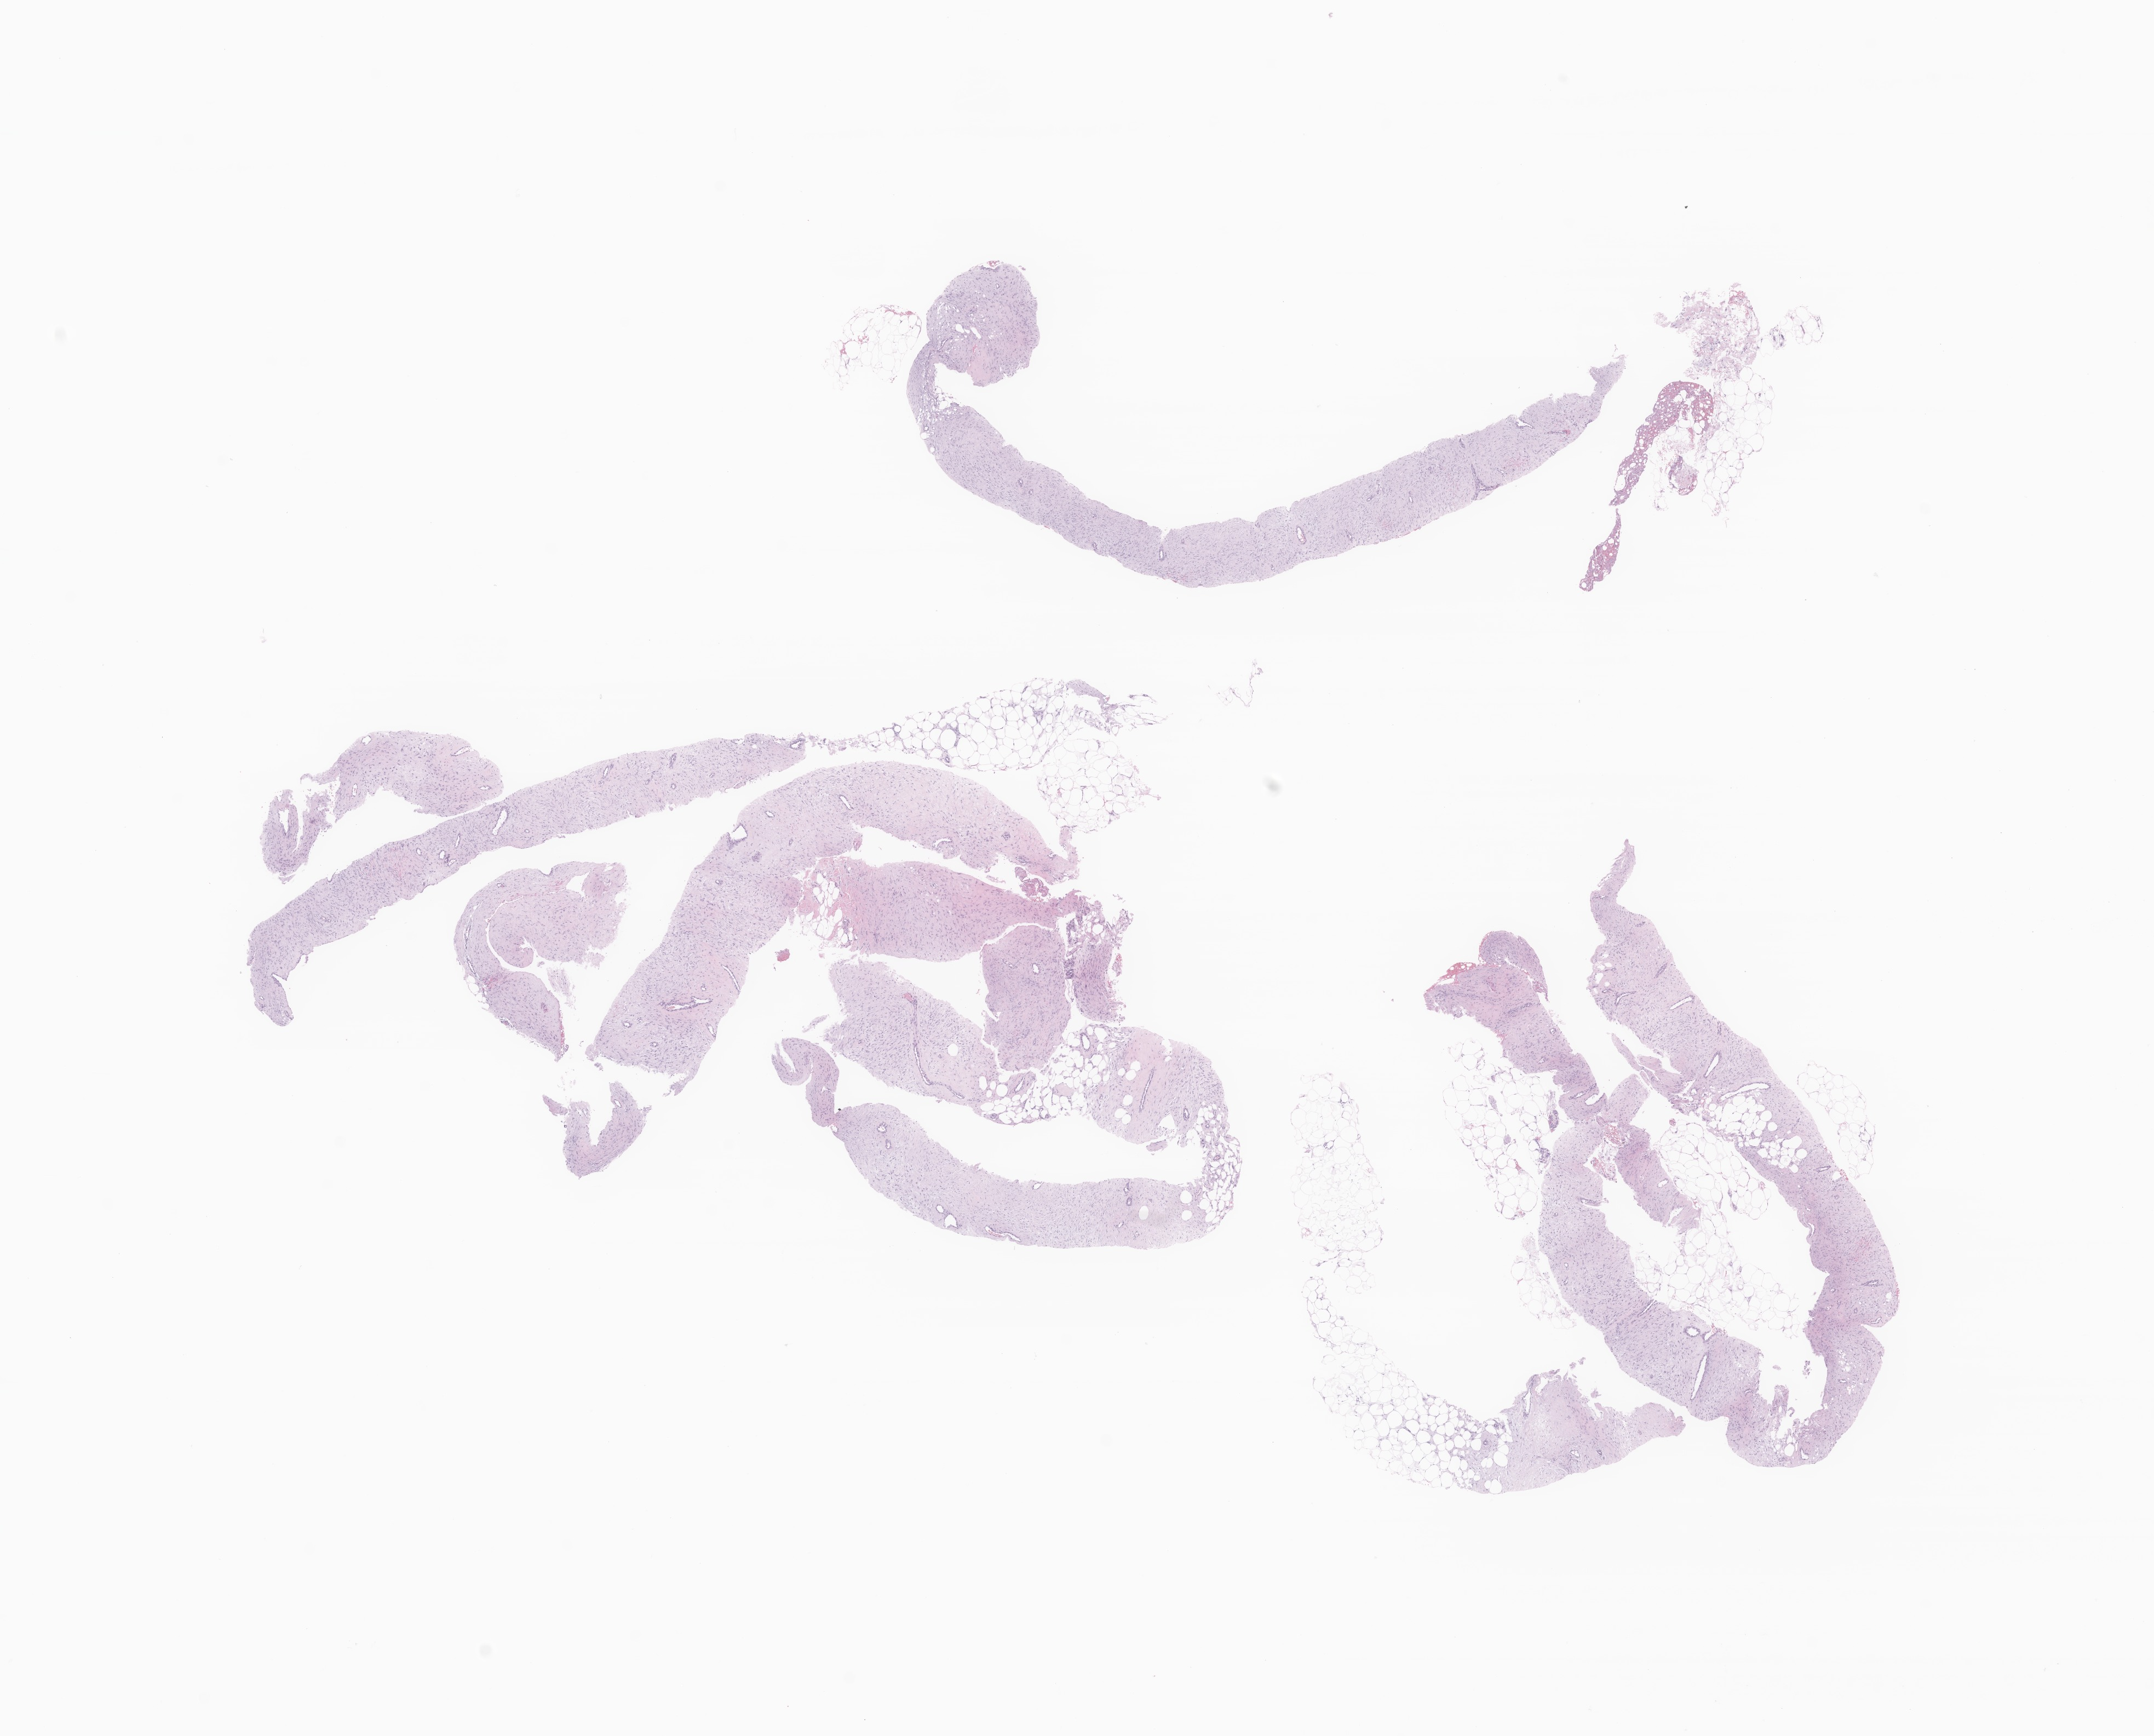
Whole-slide image, hematoxylin and eosin (H&E) stain of tumor tissue from the abdomen, a low-resolution overview of the entire scanned area, about 16.6 x 13.4 mm, formalin-fixed, paraffin-embedded (FFPE) tissue. Patient female; age 196 months (16 years 4 months).
Diagnosis: Aggressive fibromatosis.